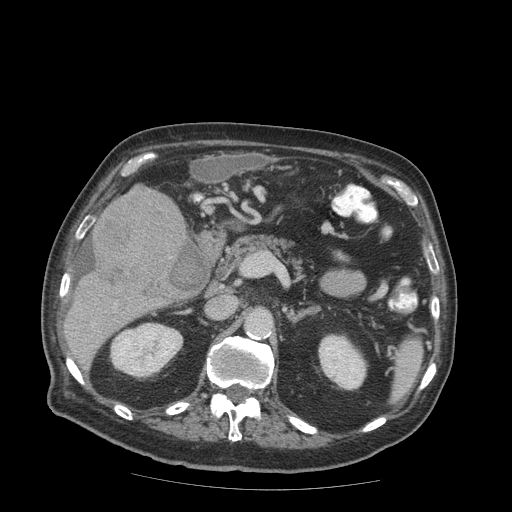
Contrast-enhanced abdominal CT (liver protocol), one axial slice; slice 37 of 99 in the series (ordered by position); reconstruction kernel STANDARD; 140 kVp; soft-tissue window (W 400 / L 40 HU); 512 × 512 image matrix, field of view 420 × 420 mm. From the clinical record (not read from this slice): diagnosis: hepatocellular carcinoma (patient treated with transarterial chemoembolisation; whether this scan precedes or follows treatment is not stated here); TNM stage (as recorded): Stage-IIIB; Child-Pugh class: A.
Outlined on this slice (semi-automatic segmentation, software-assisted and operator-edited):
- liver parenchyma outside the tumour (the mass and vessels are separate outlines, so this box may not span the whole liver): bounding box <64,190,188,346> (left, top, right, bottom; pixels)
- mass: <91,184,188,300>